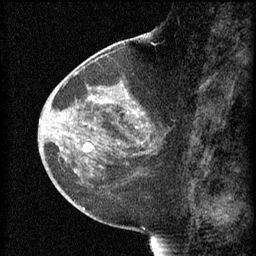
Breast MRI (dynamic contrast-enhanced), one sagittal slice; position 28 of 60 along the scan axis; 3 images stored at this slice position (order not interpretable as contrast timing); 1.5 T; TE 4.2 ms, TR 8.2 ms; 2 mm slice thickness; 256 × 256 image matrix. Female patient, age 44 years.
Annotated regions visible in this slice (semi-automatically segmented with operator editing):
- analysis volume of interest (the breast-tissue region the enhancement analysis was run in; not a lesion): box from (x=73, y=82) to (x=169, y=165) px
- tumour enhancement mask (voxels above the 70 % enhancement threshold inside the analysis volume of interest): (x=84, y=96)–(x=152, y=153)